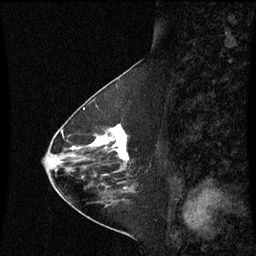
Breast MRI (dynamic contrast-enhanced), one sagittal slice; slice 26 of 60 in the series (ordered by position); dynamic contrast-enhanced series, image 2 of 3 at this slice position (ordered by acquisition); 1.5 T; TE 4.2 ms, TR 8.9 ms; 2 mm slice thickness; 256 × 256 image matrix, field of view 200 × 200 mm. Female patient, age 63 years. Case-level facts recorded for this patient, not image findings: setting: breast cancer imaged before/during neoadjuvant chemotherapy; receptor status: HR-positive, HER2-negative.
Outlined on this slice (semi-automatic segmentation, software-assisted and operator-edited):
- analysis volume of interest (the breast-tissue region the enhancement analysis was run in; not a lesion): bounding box <94,124,130,177> (left, top, right, bottom; pixels)
- tumour enhancement mask (voxels above the 70 % enhancement threshold inside the analysis volume of interest): <95,124,129,161>